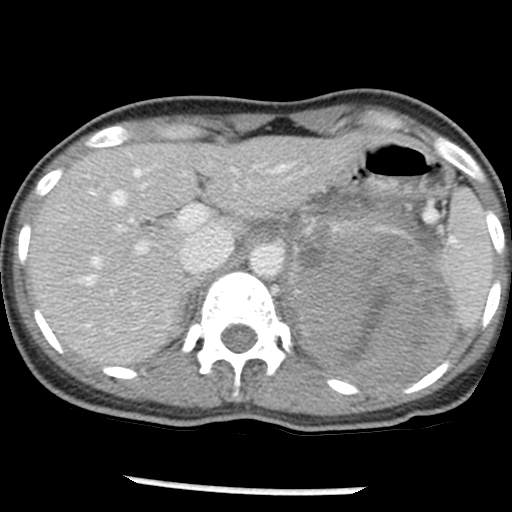
Contrast-enhanced abdominal CT, one axial slice. Position 34 of 54 along the scan axis. Reconstruction kernel STANDARD. 120 kVp. Intravenous contrast given. Soft-tissue window (W 400 / L 40 HU). 5 mm slice thickness. 512 × 512 image matrix, field of view 240 × 240 mm. Female patient, age 33 years. Case-level facts recorded for this patient, not image findings: diagnosis: adrenocortical carcinoma; tumour side: left adrenal; tumour size at pathology: 11 cm; Ki-67 index: 20 %; stage (as recorded): 2.
Structures marked on this image (semi-automatic segmentation, software-assisted and operator-edited):
- mass: box from (x=288, y=203) to (x=453, y=385) px